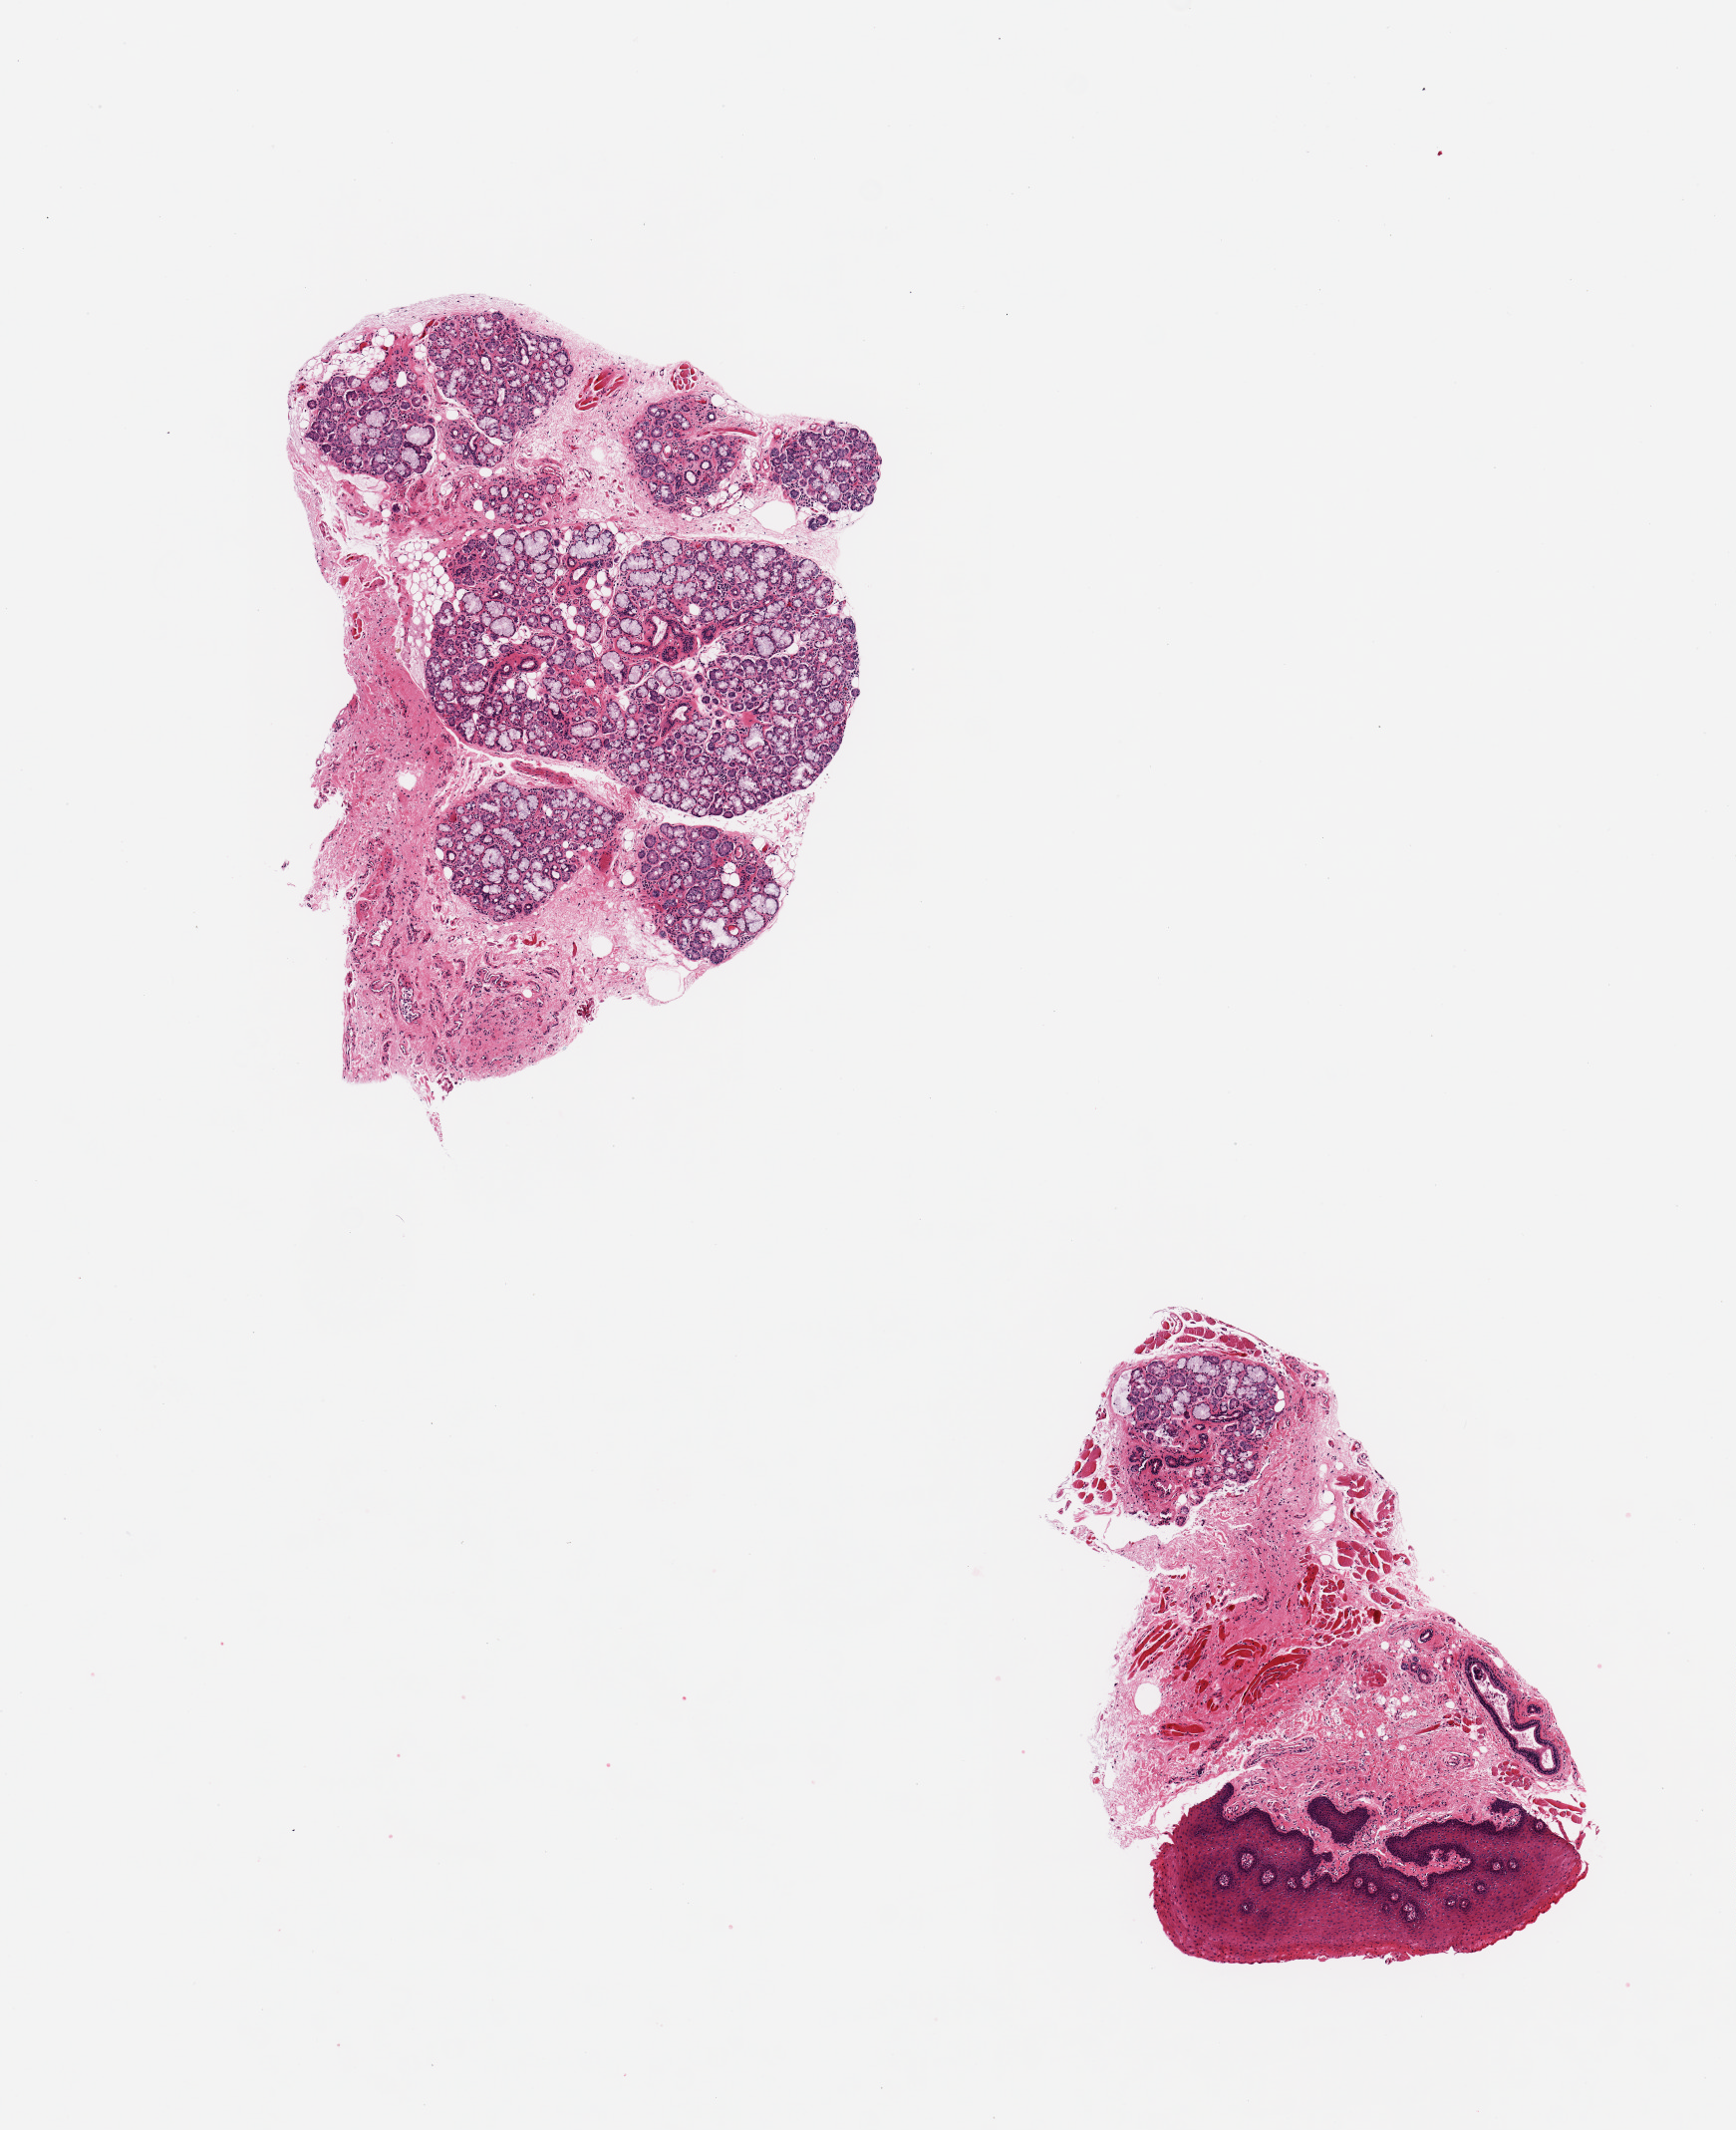
Haematoxylin and eosin whole-slide image — low-resolution overview of the scanned area, about 6.9 x 8.5 mm, PAXgene-fixed paraffin-embedded (PFPE) section, sampled site (target tissue): minor salivary gland, donor tissue sample.
Reviewer comment on this tissue sample: 2 pieces; one has 20% stroma; other has 20% glands, 80% skin and stroma.